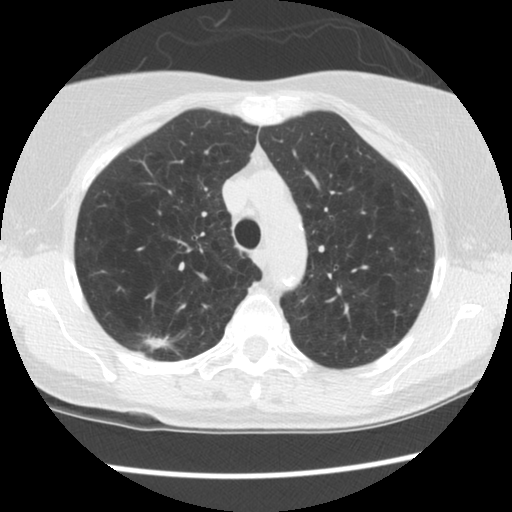
Low-dose screening chest CT, one axial slice; slice 103 of 134 in the series (ordered by position); 120 kVp; lung window (W 1500 / L -600 HU); 2.5 mm slice thickness; 512 × 512 image matrix, field of view 319 × 319 mm.
Outlined on this slice (outlined manually by an expert reader):
- lesion 1 (tumor, upper lobe of right lung): bounding box <143,335,171,349> (left, top, right, bottom; pixels)